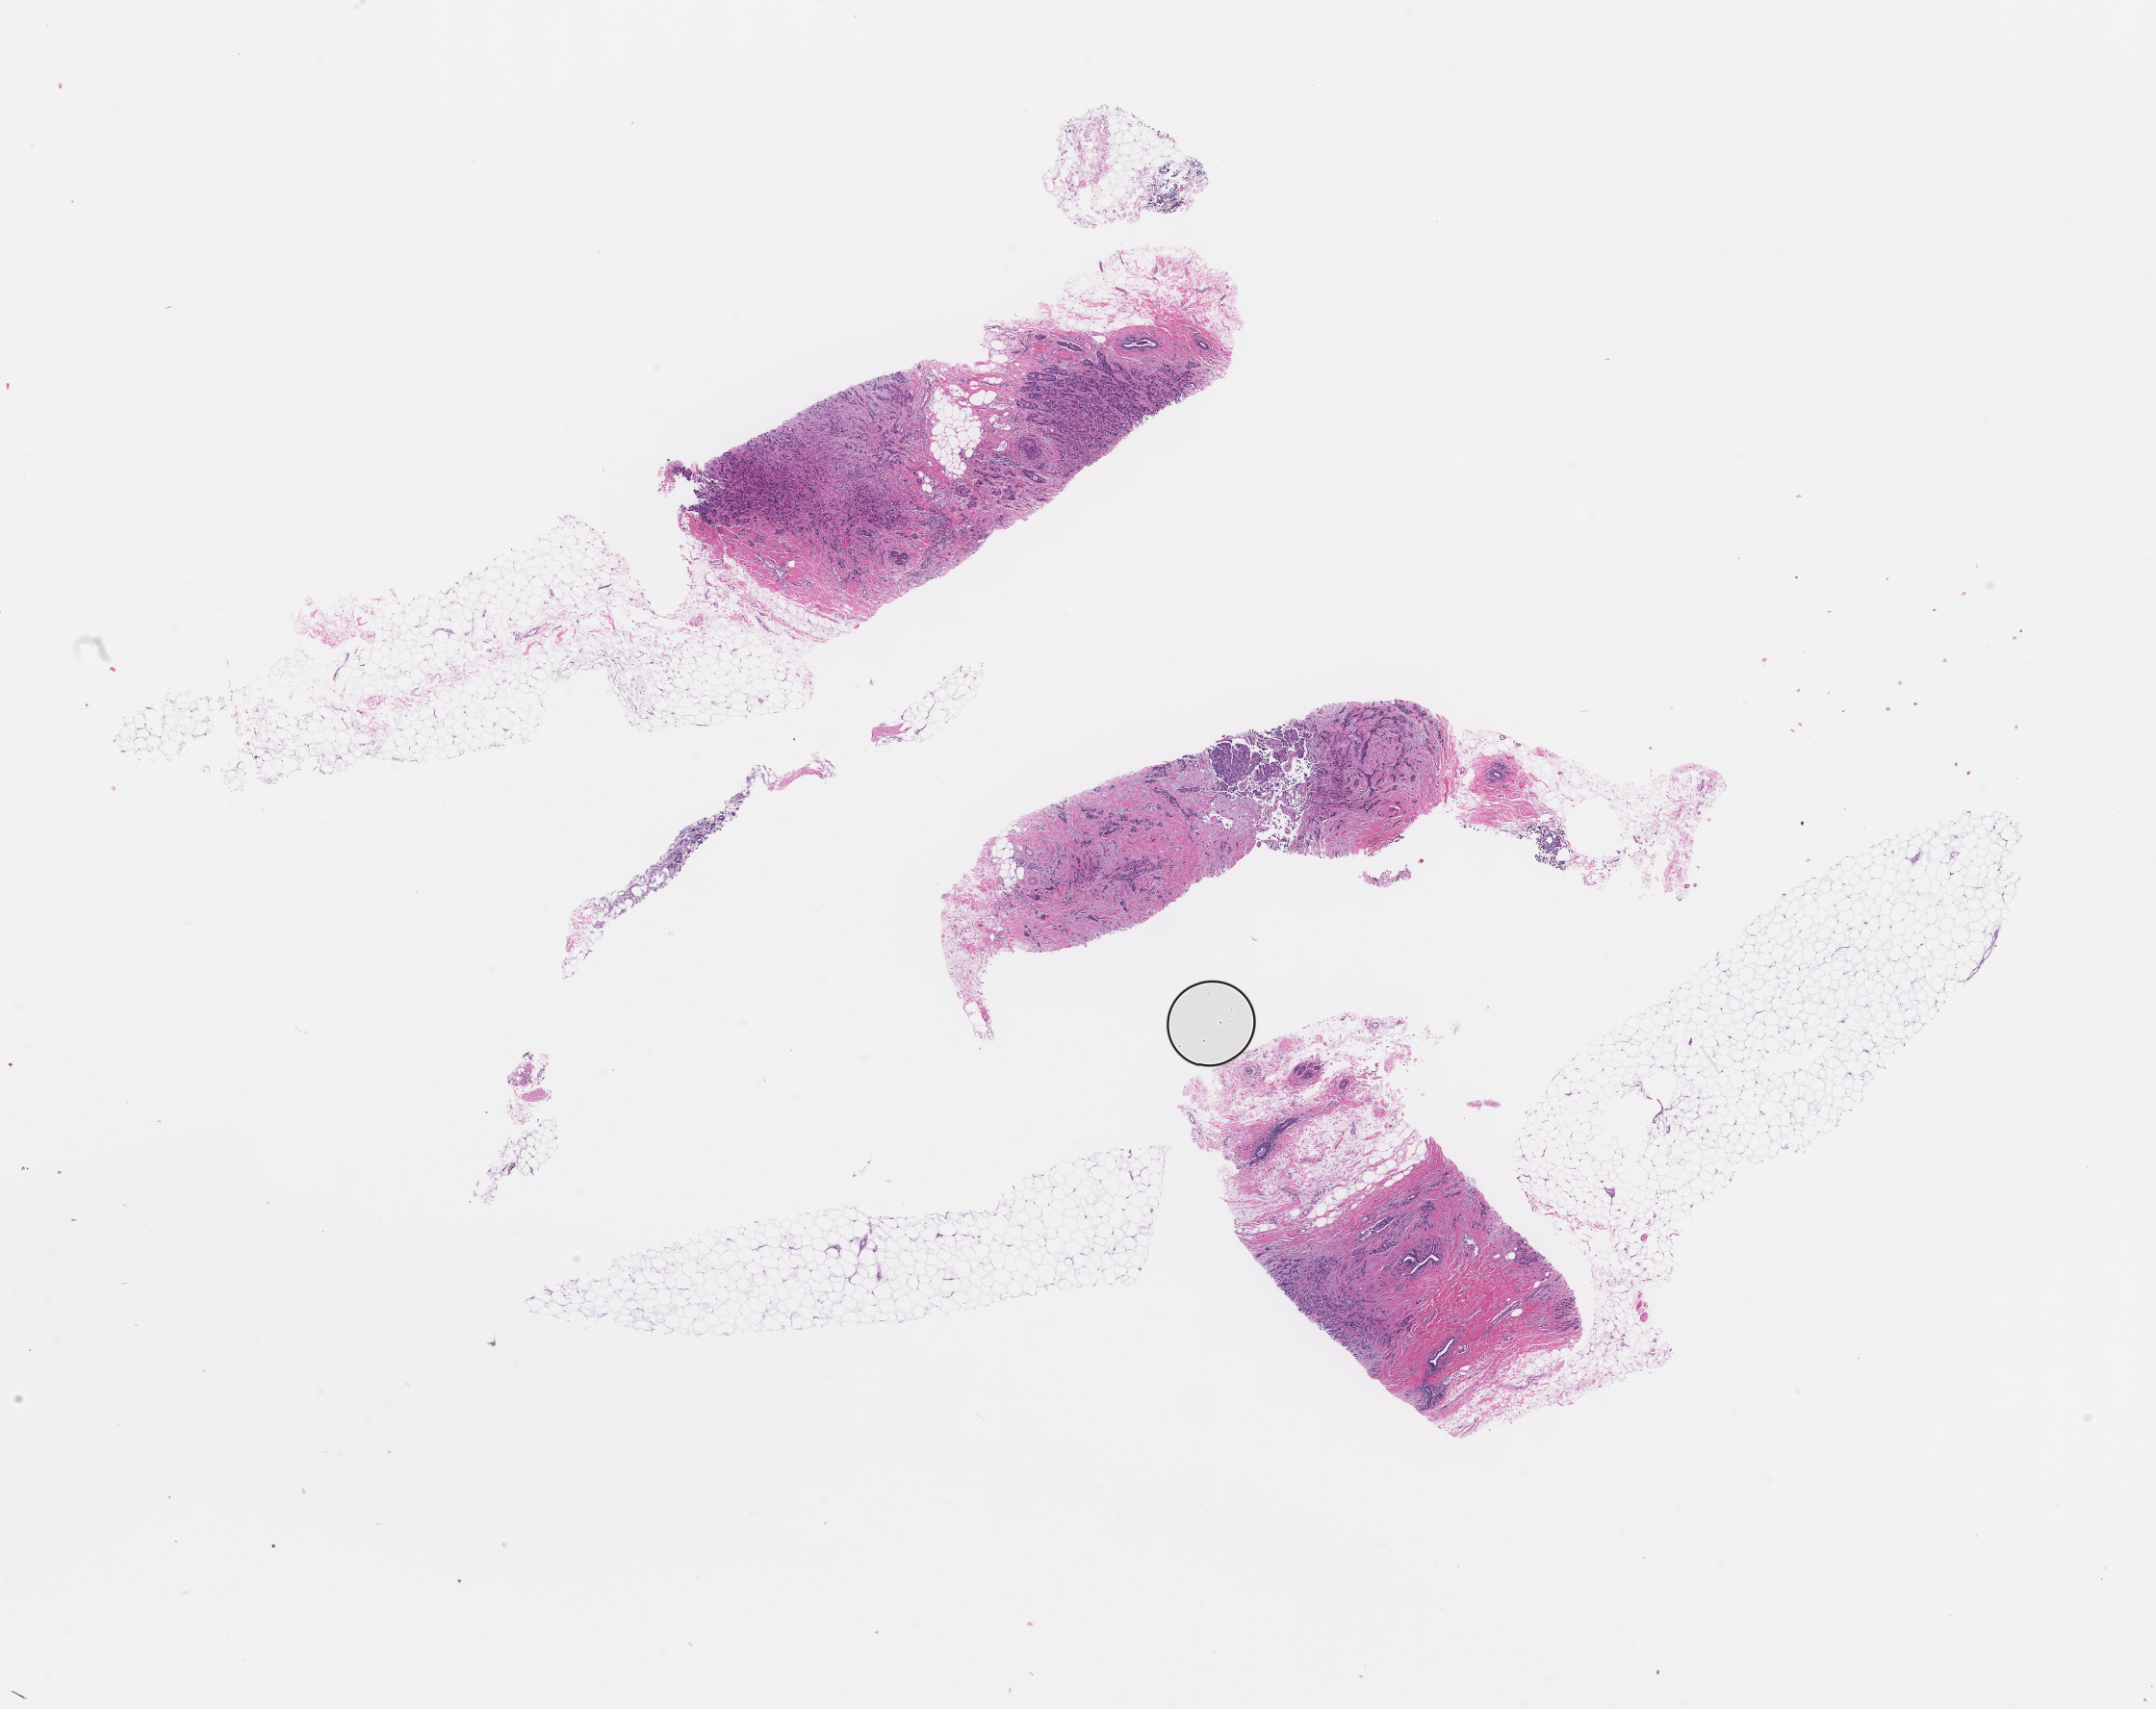
Whole-slide image, hematoxylin and eosin (H&E) stain — a low-resolution overview of the entire scanned area, about 18.1 x 14.3 mm. Formalin-fixed, paraffin-embedded (FFPE) tissue. Site: breast. Specimen time point: archival tissue. Female patient.
• this section: primary tumour tissue
• diagnosis: Invasive Breast Carcinoma